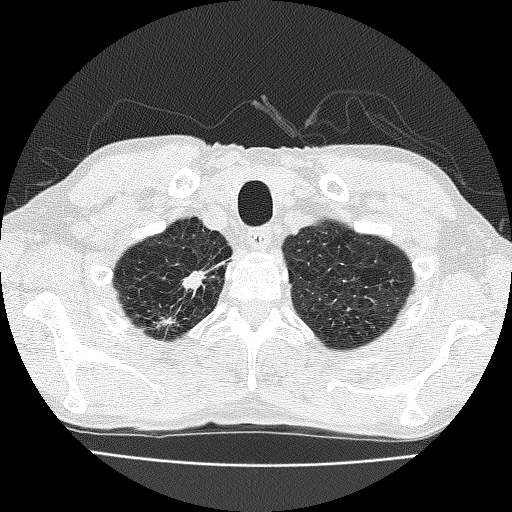
Low-dose screening chest CT, axial slice; third screening round (two years after baseline); lung window (W 1500 / L -600 HU); 2 mm slice thickness; 120 kVp; slice 28 of 185 in the series. Male, age 63 years at enrolment.
• Lesion marked by an expert reader, bounding box (x1, y1, x2, y2) in pixels: (145, 257, 225, 334).
• Screening reader's record for this exam (one nodule recorded; not confirmed to be the boxed lesion): non-calcified nodule or mass ≥4 mm, right upper lobe, 17 × 10 mm, spiculated (stellate) margins, soft tissue attenuation, pre-existing on the prior screen: yes; interval growth: yes.
• Official screen result: positive, other.
• Later outcome: lung cancer diagnosed 28 days after this screen — adenocarcinoma, NOS, right upper lobe, moderately differentiated (G2), stage IIIB (AJCC 6th edition), 17 mm at pathology.